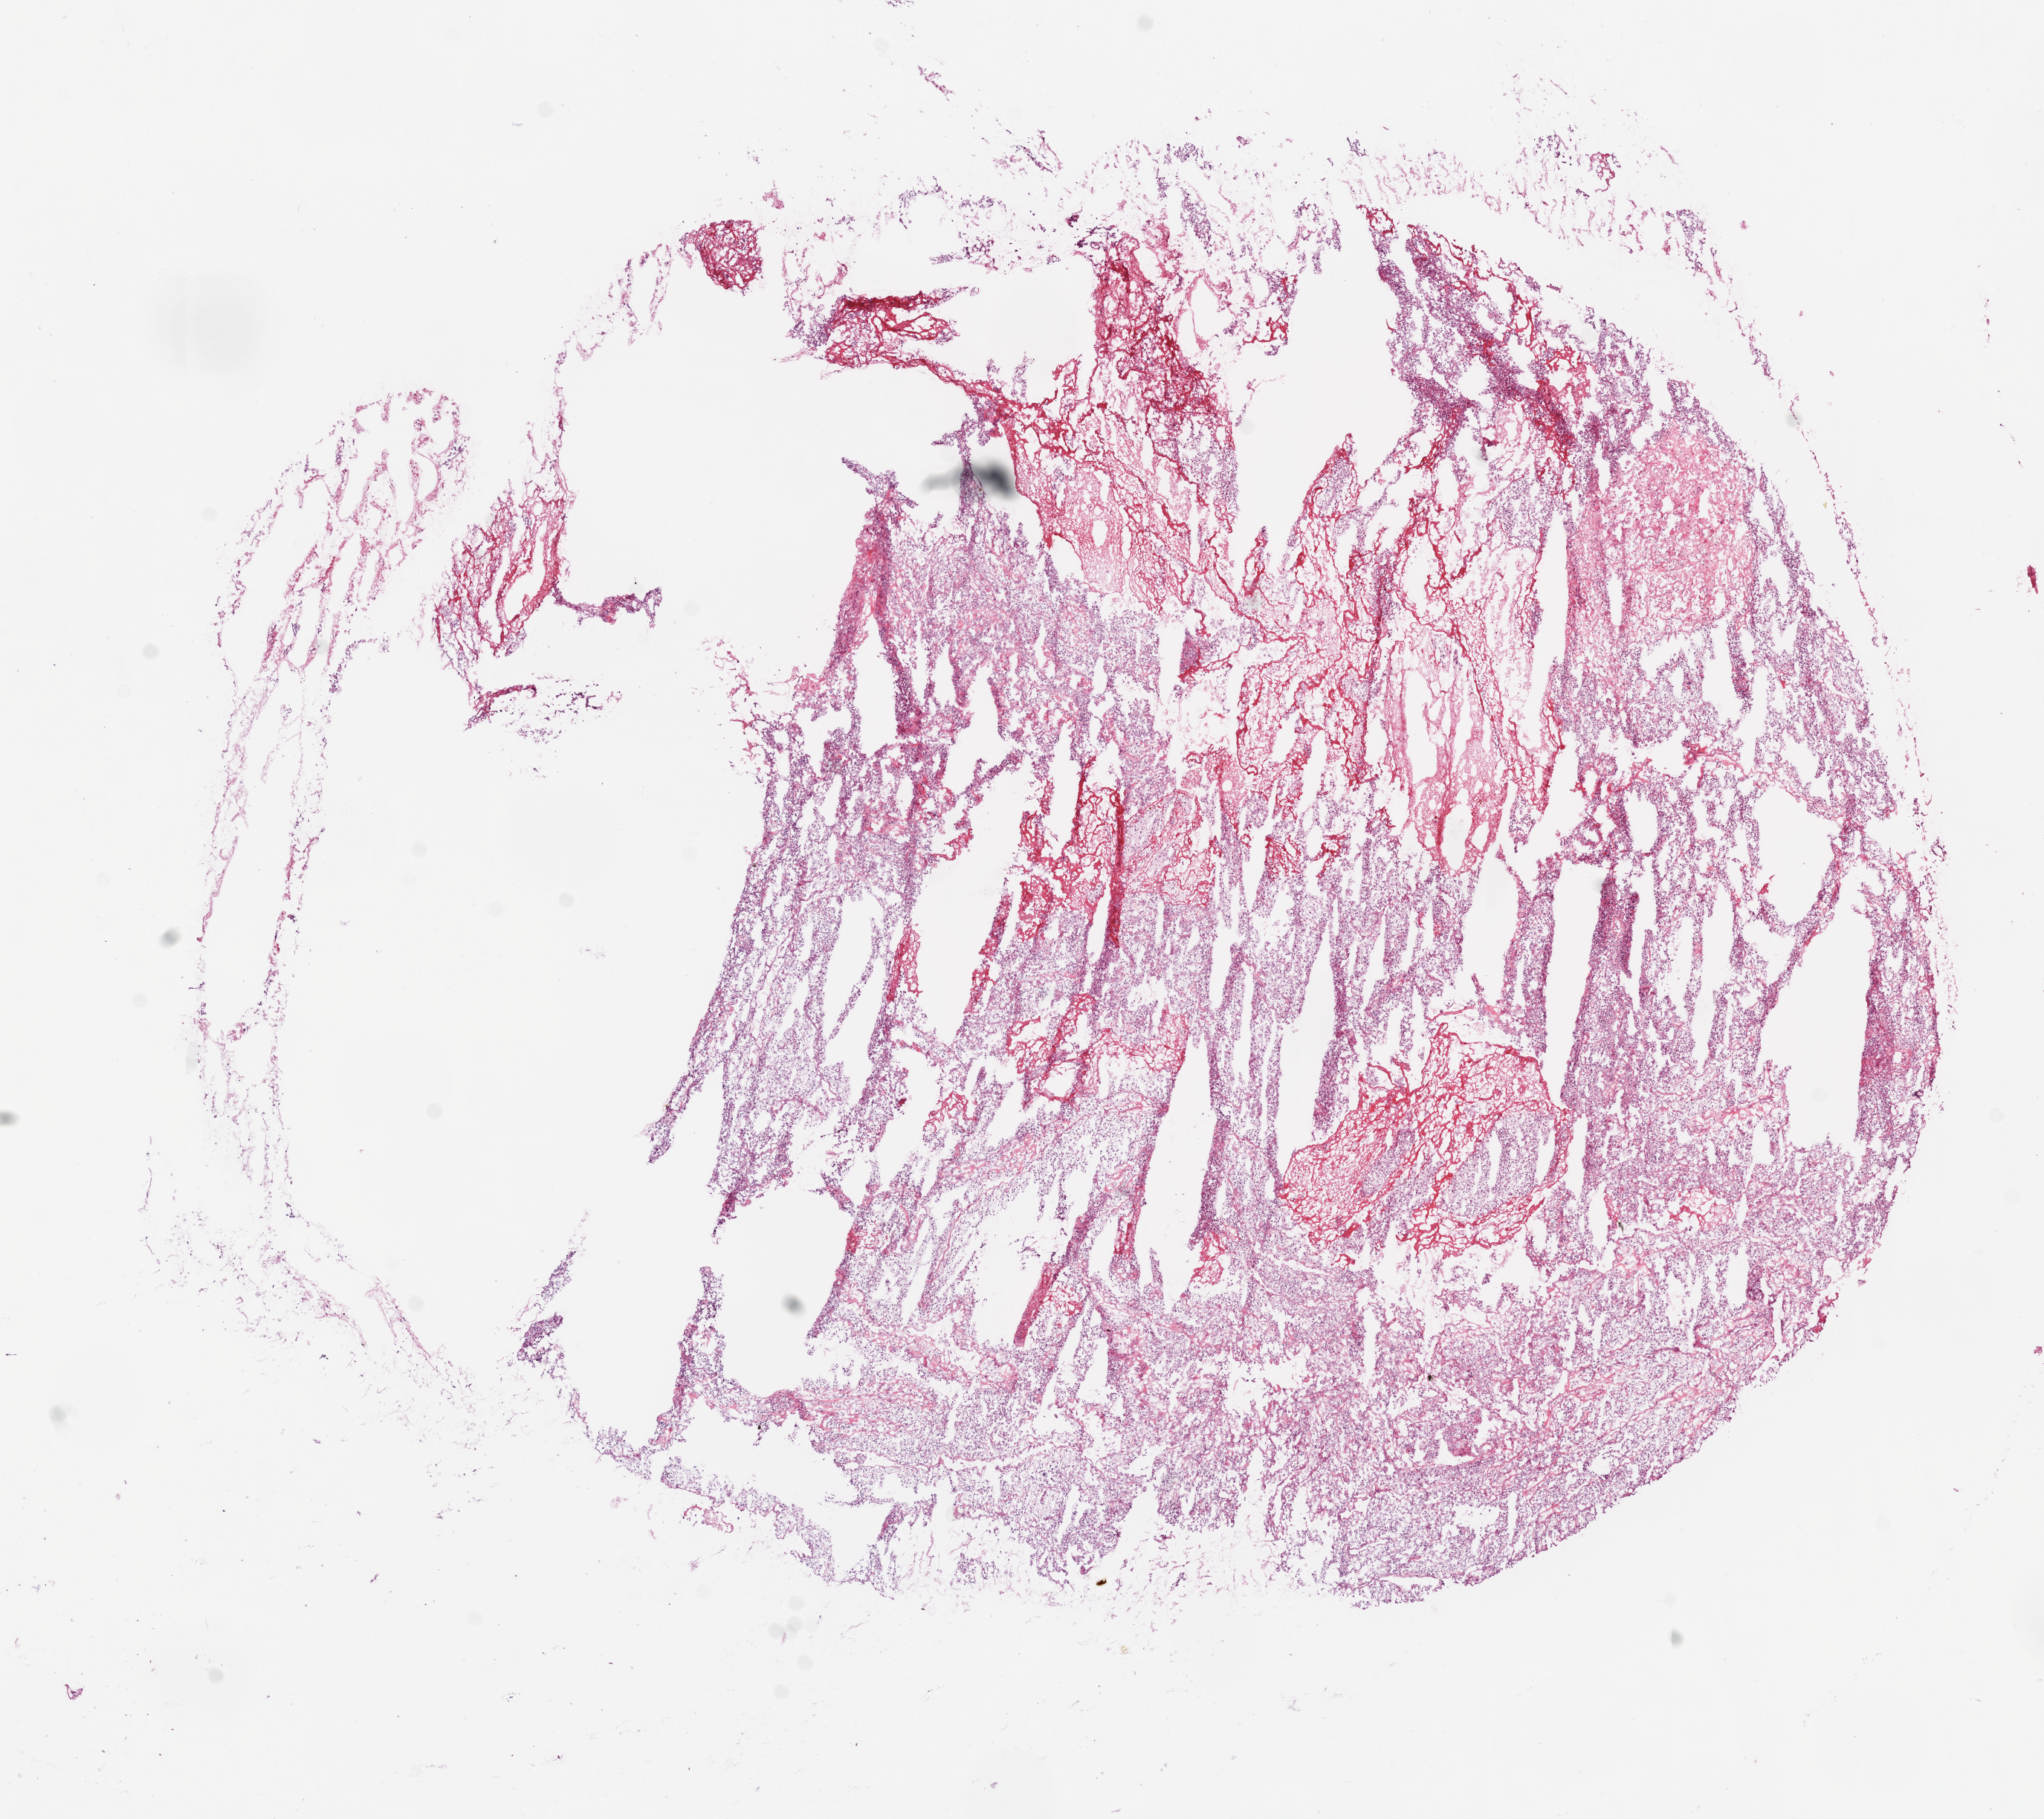
Digitized H&E-stained tissue section (whole slide), a low-resolution overview of the entire scanned area, about 11.0 x 9.8 mm (from a 20x scan). Frozen section. Sample: primary tumour, kidney. Patient: female, age at initial diagnosis 70 years. Histologic grade: G2 (moderately differentiated). Pathologist review of this section (percent, as recorded): tumour cells 85%, tumour nuclei 85%, normal cells 0%, stromal cells 15%, necrosis 0%.
Lymph nodes positive (case pathology): 0 of 2 examined. Pathologic diagnosis: Clear cell adenocarcinoma, NOS. AJCC pathologic stage: III (7th edition).